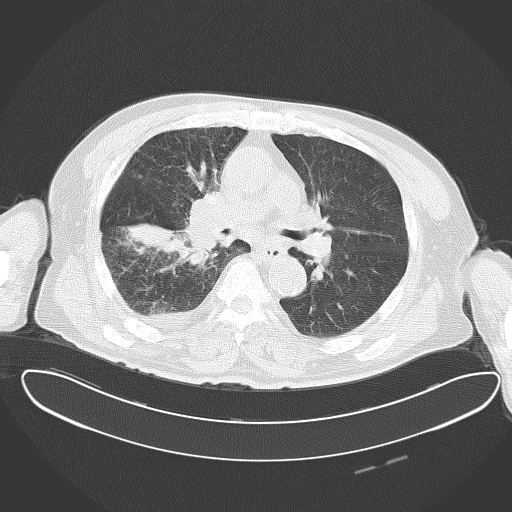
Chest CT, one axial slice. Position 34 of 62 along the scan axis. 120 kVp. Lung window (W 1500 / L -600 HU). 512 × 512 image matrix, field of view 427 × 427 mm. Male patient, age 78 years. Case-level facts recorded for this patient, not image findings: clinical TNM (as recorded): T2 N1 M1.
Annotated regions visible in this slice (rectangle marked by the reading radiologist):
- lung tumour (recorded histology: adenocarcinoma): bounding box [x1, y1, x2, y2] px = [128, 186, 225, 269]